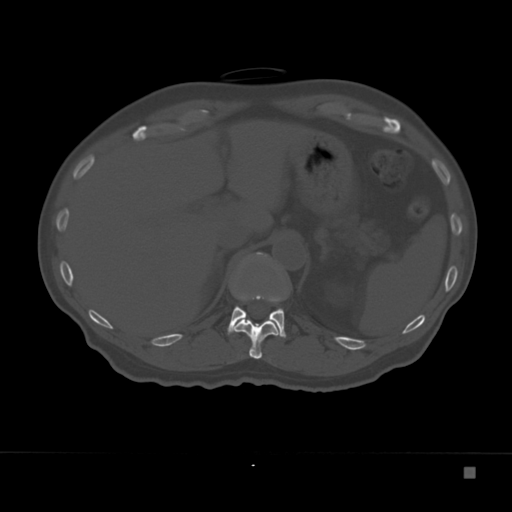
CT including the spine, one axial slice; position 143 of 332 along the scan axis; reconstruction kernel Br40s; 120 kVp; bone window (W 1800 / L 400 HU); 1.5 mm slice thickness; 512 × 512 image matrix, field of view 389 × 389 mm. Male patient, age 72 years. Case-level facts recorded for this patient, not image findings: primary cancer: skeletal.
Structures marked on this image (semi-automatically segmented with operator editing):
- T11 vertebra: bounding box [x1, y1, x2, y2] px = [230, 293, 283, 359]
- T12 vertebra: [227, 252, 286, 338]